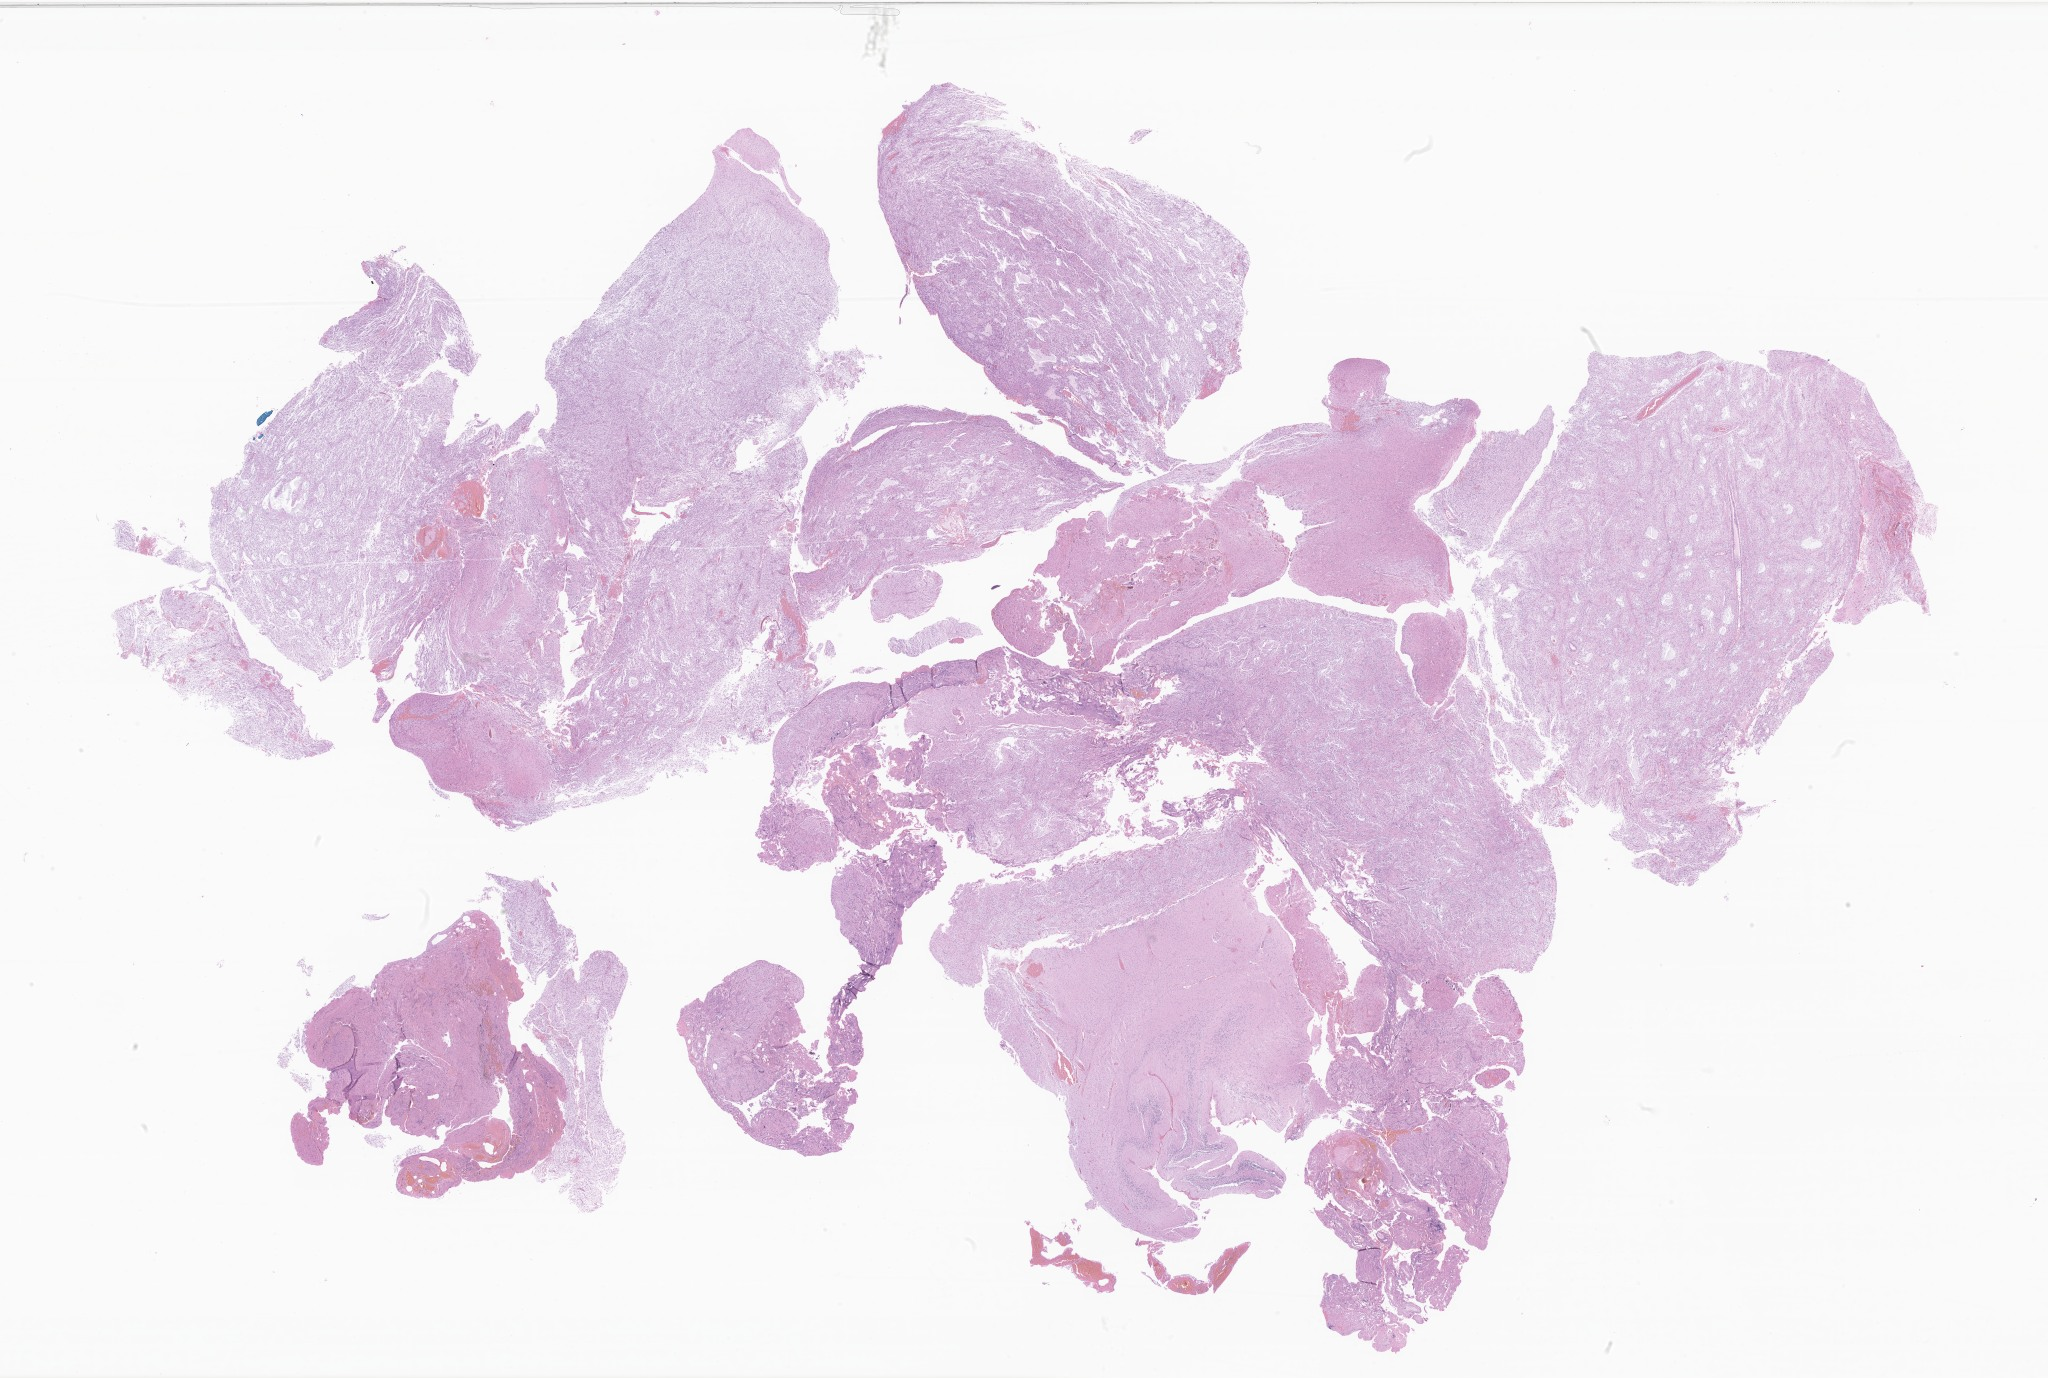
Digitized hematoxylin and eosin (H&E)-stained section of tumor tissue from the brain — shown as a low-resolution overview of the whole scanned area (about 34.5 x 23.2 mm); formalin-fixed, paraffin-embedded (FFPE) tissue. Male patient, age 60 months (5 years).
- diagnosis (ICD-O-3 morphology term): Pilocytic astrocytoma